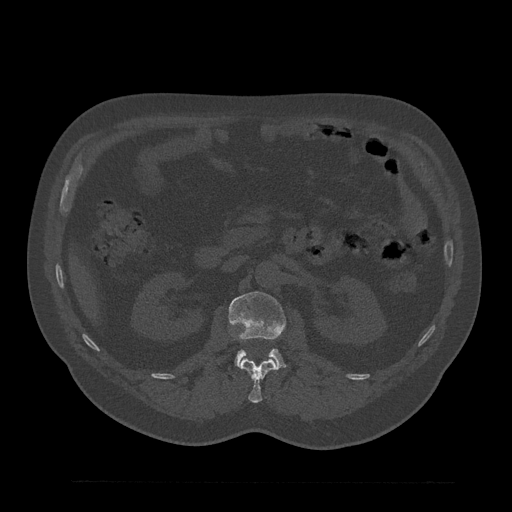
CT including the spine, one axial slice; reconstruction kernel Br40s/3; 120 kVp; bone window (W 1800 / L 400 HU); 0.5 mm slice thickness; 512 × 512 image matrix, field of view 430 × 430 mm. Male patient, age 61 years. Case-level facts recorded for this patient, not image findings: primary cancer: prostate.
Outlined on this slice (semi-automatically segmented with operator editing):
- L1 vertebra: bounding box <240,359,278,403> (left, top, right, bottom; pixels)
- L2 vertebra: <229,291,285,368>